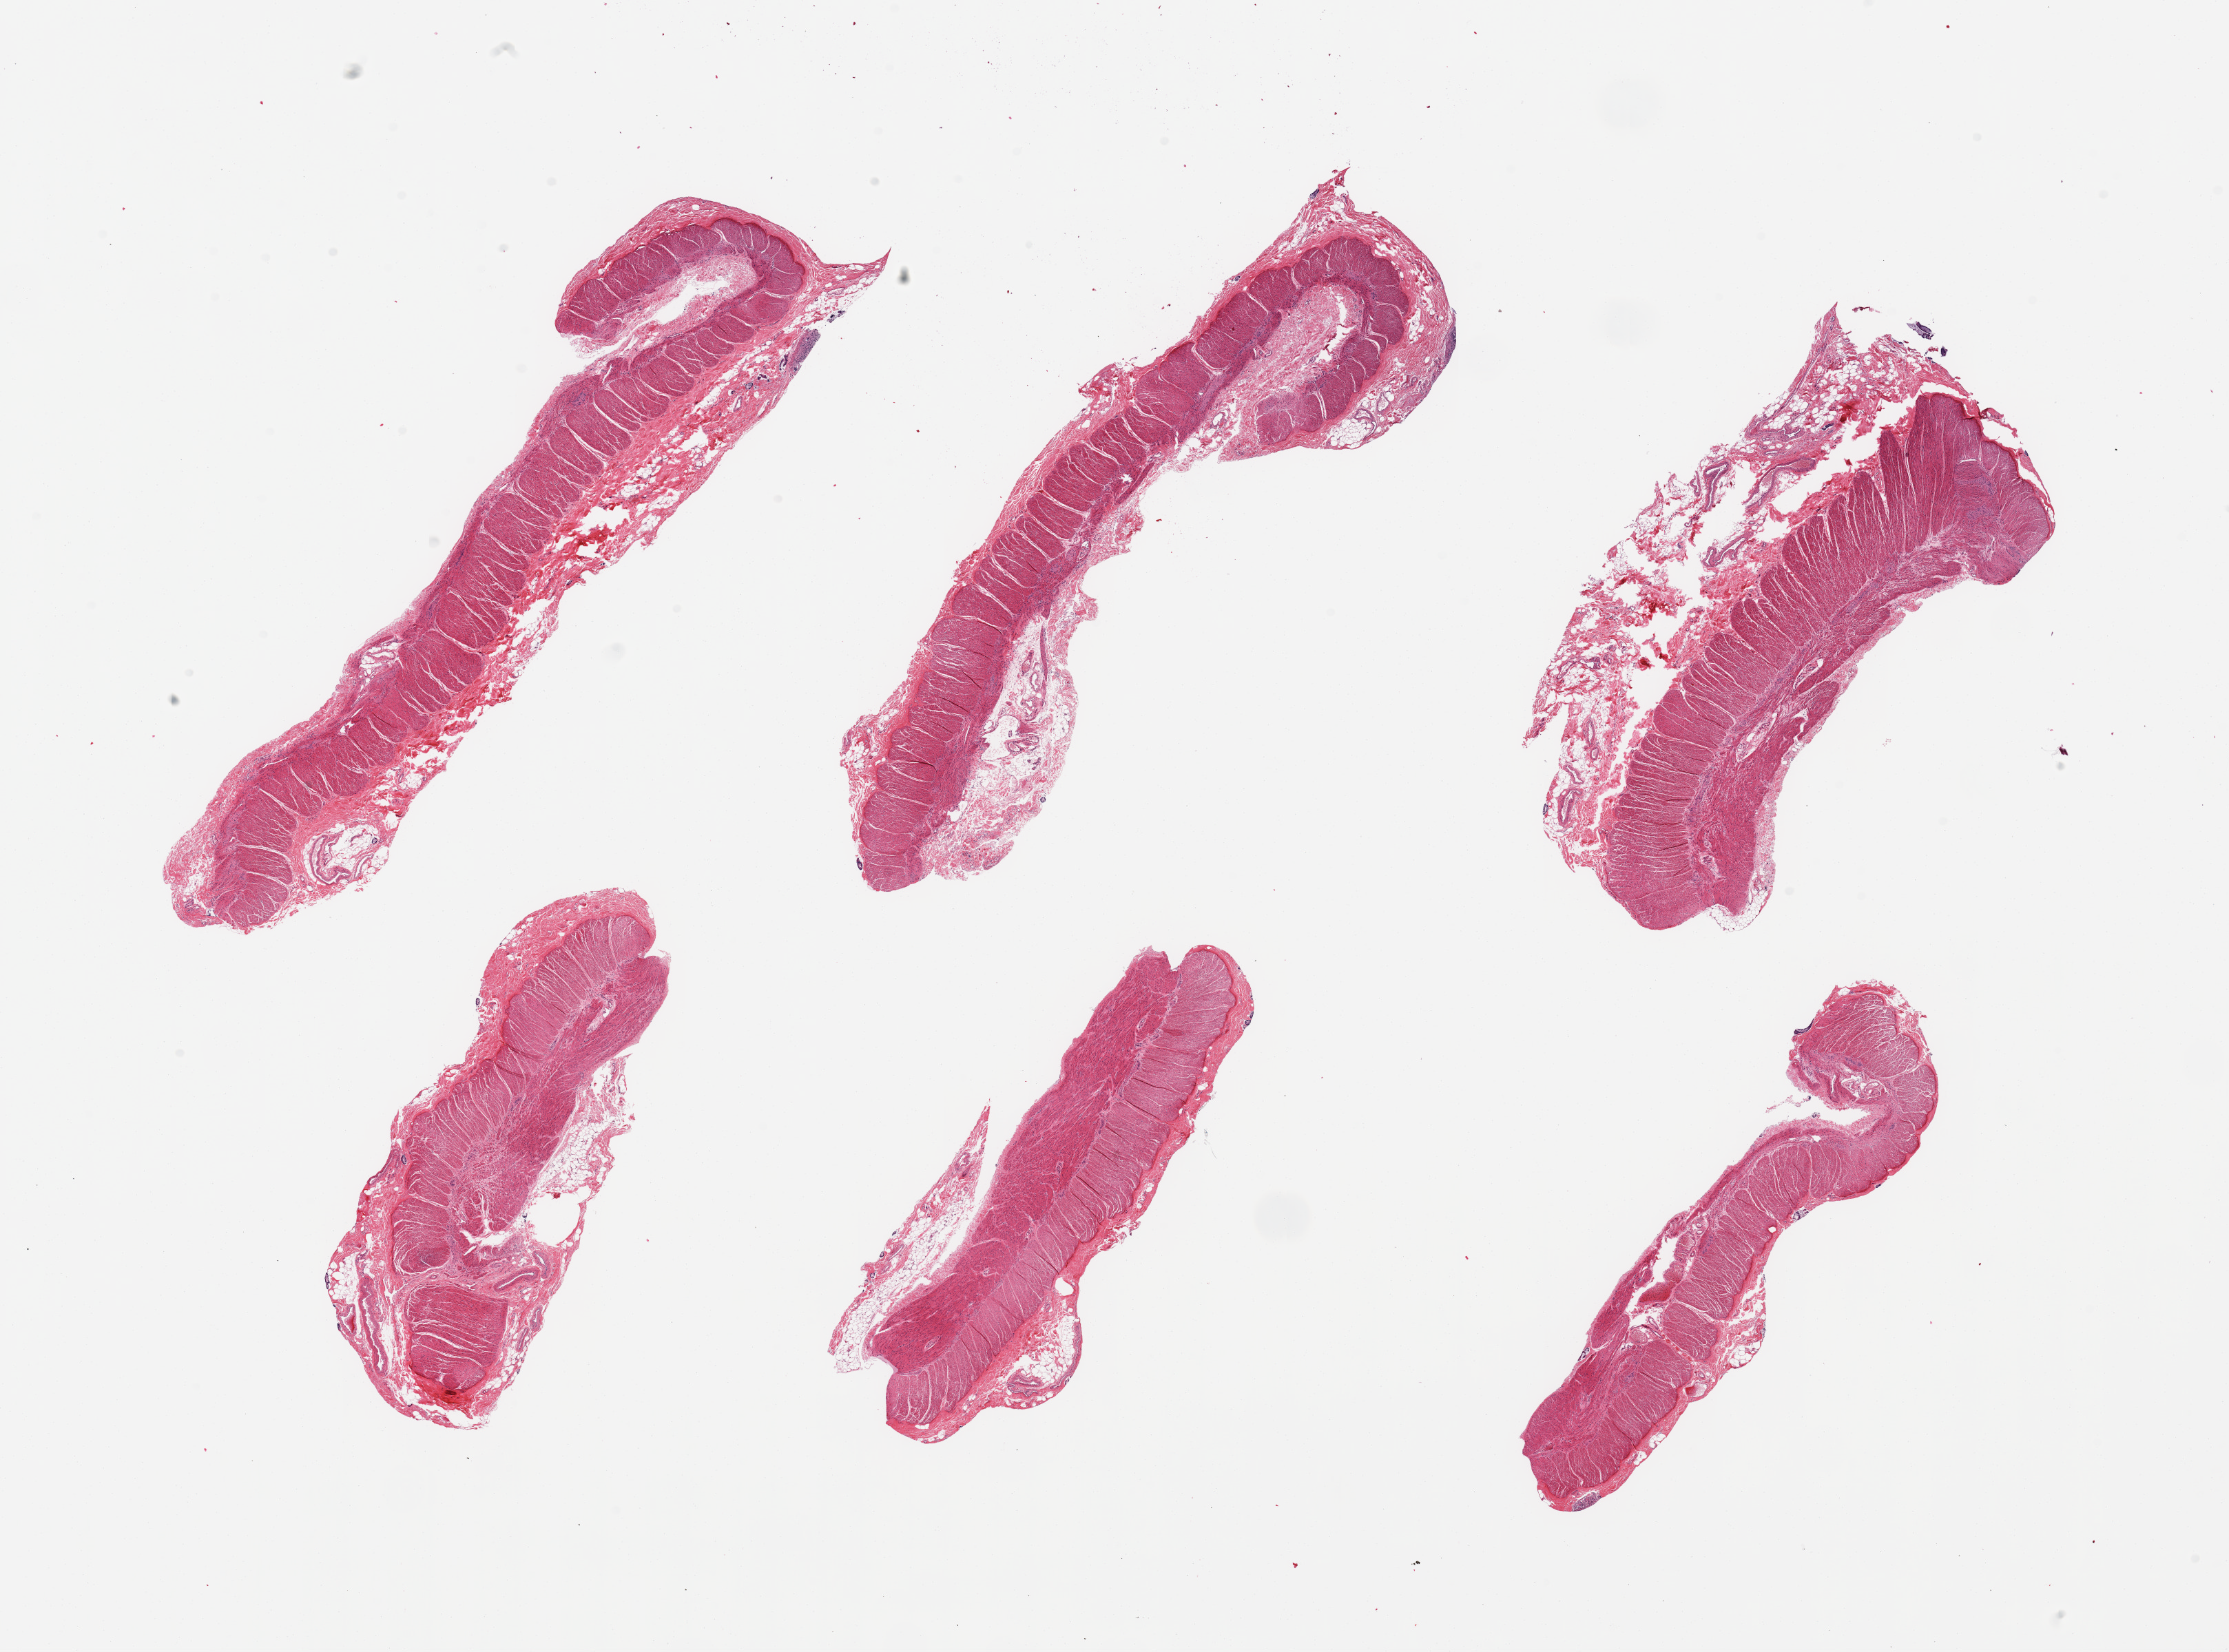
Digitized hematoxylin and eosin (H&E)-stained section — whole scanned area (about 25.6 x 19.0 mm, acquisition: 20x scan) shown as a low-resolution overview, PAXgene-fixed, paraffin-embedded tissue, target tissue: transverse colon, tissue donor sample. Male donor.
Reviewer comment on this tissue sample: 6 pieces; muscularis (target is full thickness) - can be compared to sigmoid colon specimen.